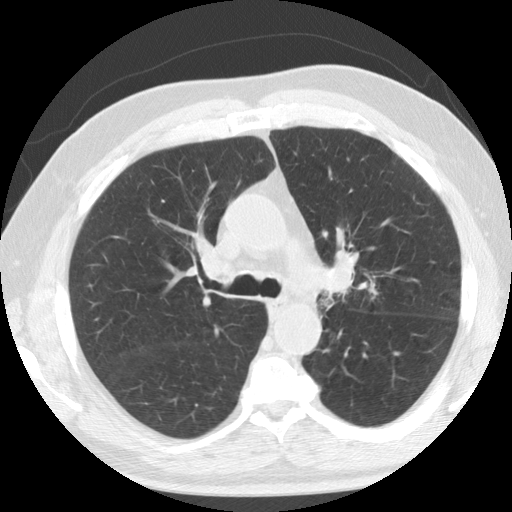
Chest CT (low-dose screening protocol), one axial image. Second annual screen. Lung window (W 1500 / L -600 HU). 2.5 mm slice thickness. Standard (soft-tissue) reconstruction kernel (STANDARD). Male, age 74 years at enrolment.
Lesion marked by an expert reader, box from (x=302, y=248) to (x=368, y=315) px. Screening reader's record for this exam: no non-calcified nodule ≥4 mm recorded. Official screen result: positive, other. Later outcome: lung cancer diagnosed 274 days after this screen — non-small cell carcinoma, left upper lobe, poorly differentiated (G3), stage IIB (AJCC 6th edition).